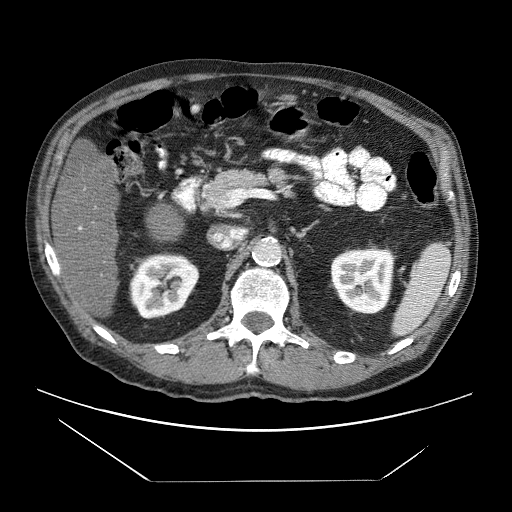
Contrast-enhanced abdominal CT (liver protocol), one axial slice. Position 24 of 83 along the scan axis. Reconstruction kernel STANDARD. 120 kVp. Soft-tissue window (W 400 / L 40 HU). 2.5 mm slice thickness. 512 × 512 image matrix. From the clinical record (not read from this slice): diagnosis: hepatocellular carcinoma (patient treated with transarterial chemoembolisation; whether this scan precedes or follows treatment is not stated here); TNM stage (as recorded): Stage-IVB; Child-Pugh class: B; tumour nodularity: uninodular.
Annotated regions visible in this slice (semi-automatically segmented with operator editing):
- liver parenchyma outside the tumour (the mass and vessels are separate outlines, so this box may not span the whole liver): bounding box [x1, y1, x2, y2] px = [52, 156, 118, 316]
- liver vessels: [79, 227, 82, 230]